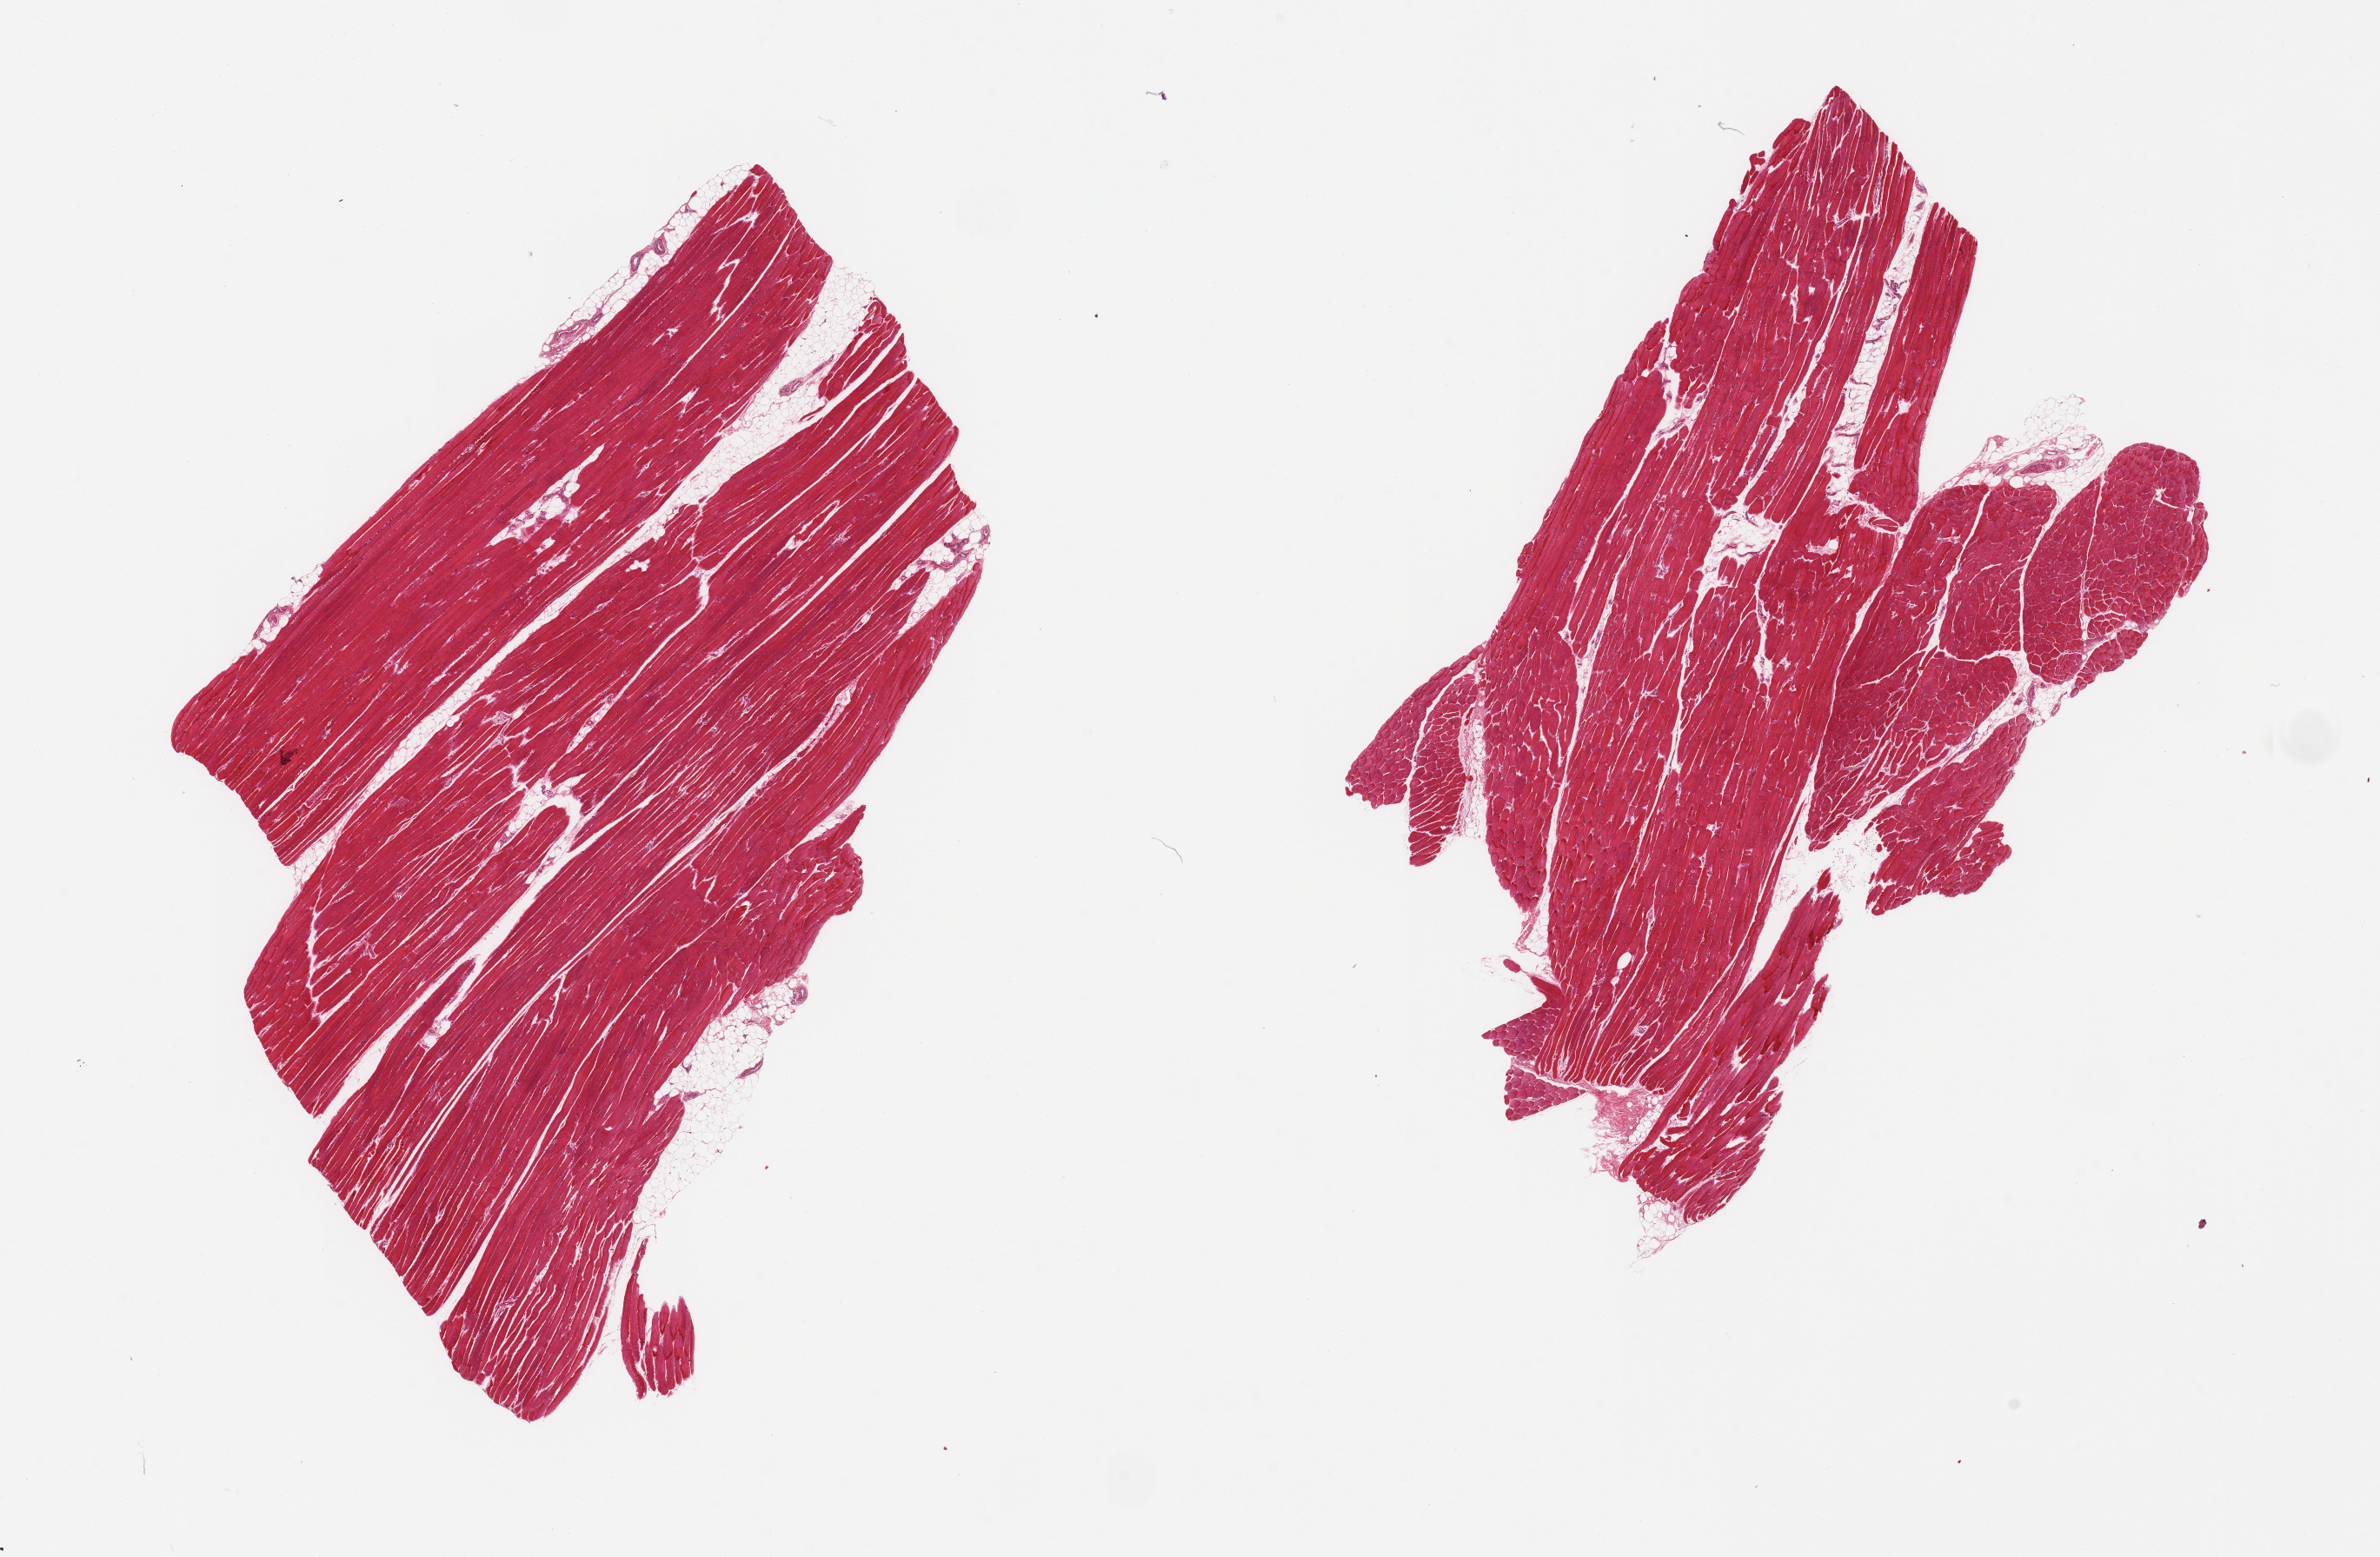
Whole-slide image, haematoxylin and eosin stain — a low-resolution overview of the entire scanned area, about 21.7 x 14.2 mm (slide scanned at 20x); PAXgene-fixed, paraffin-embedded tissue; sampled site (target tissue): skeletal muscle; tissue donor sample.
* reviewer comment on this tissue sample: 2 pieces, ~5-10% interstitial fat